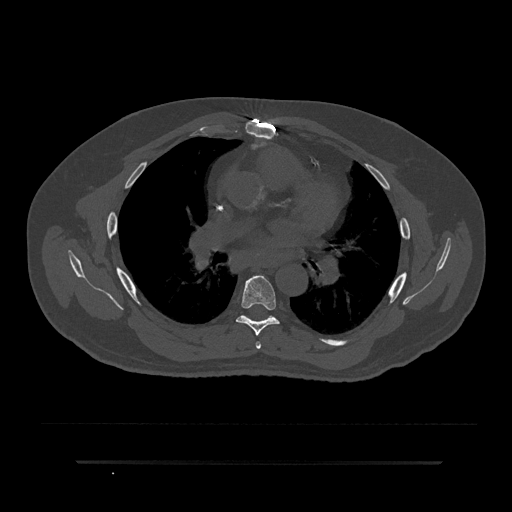
CT including the spine, one axial slice. Slice 524 of 797 in the series (ordered by position). Reconstruction kernel Br40s/3. Bone window (W 1800 / L 400 HU). 0.5 mm slice thickness. 512 × 512 image matrix, field of view 464 × 464 mm. Male patient, age 59 years. Case-level facts recorded for this patient, not image findings: primary cancer: bile ducts; vertebrae with lytic lesions (as recorded): T10.
Annotated regions visible in this slice (semi-automatic segmentation, software-assisted and operator-edited):
- T5 vertebra: bounding box [x1, y1, x2, y2] px = [255, 342, 261, 349]
- T6 vertebra: [236, 275, 280, 336]